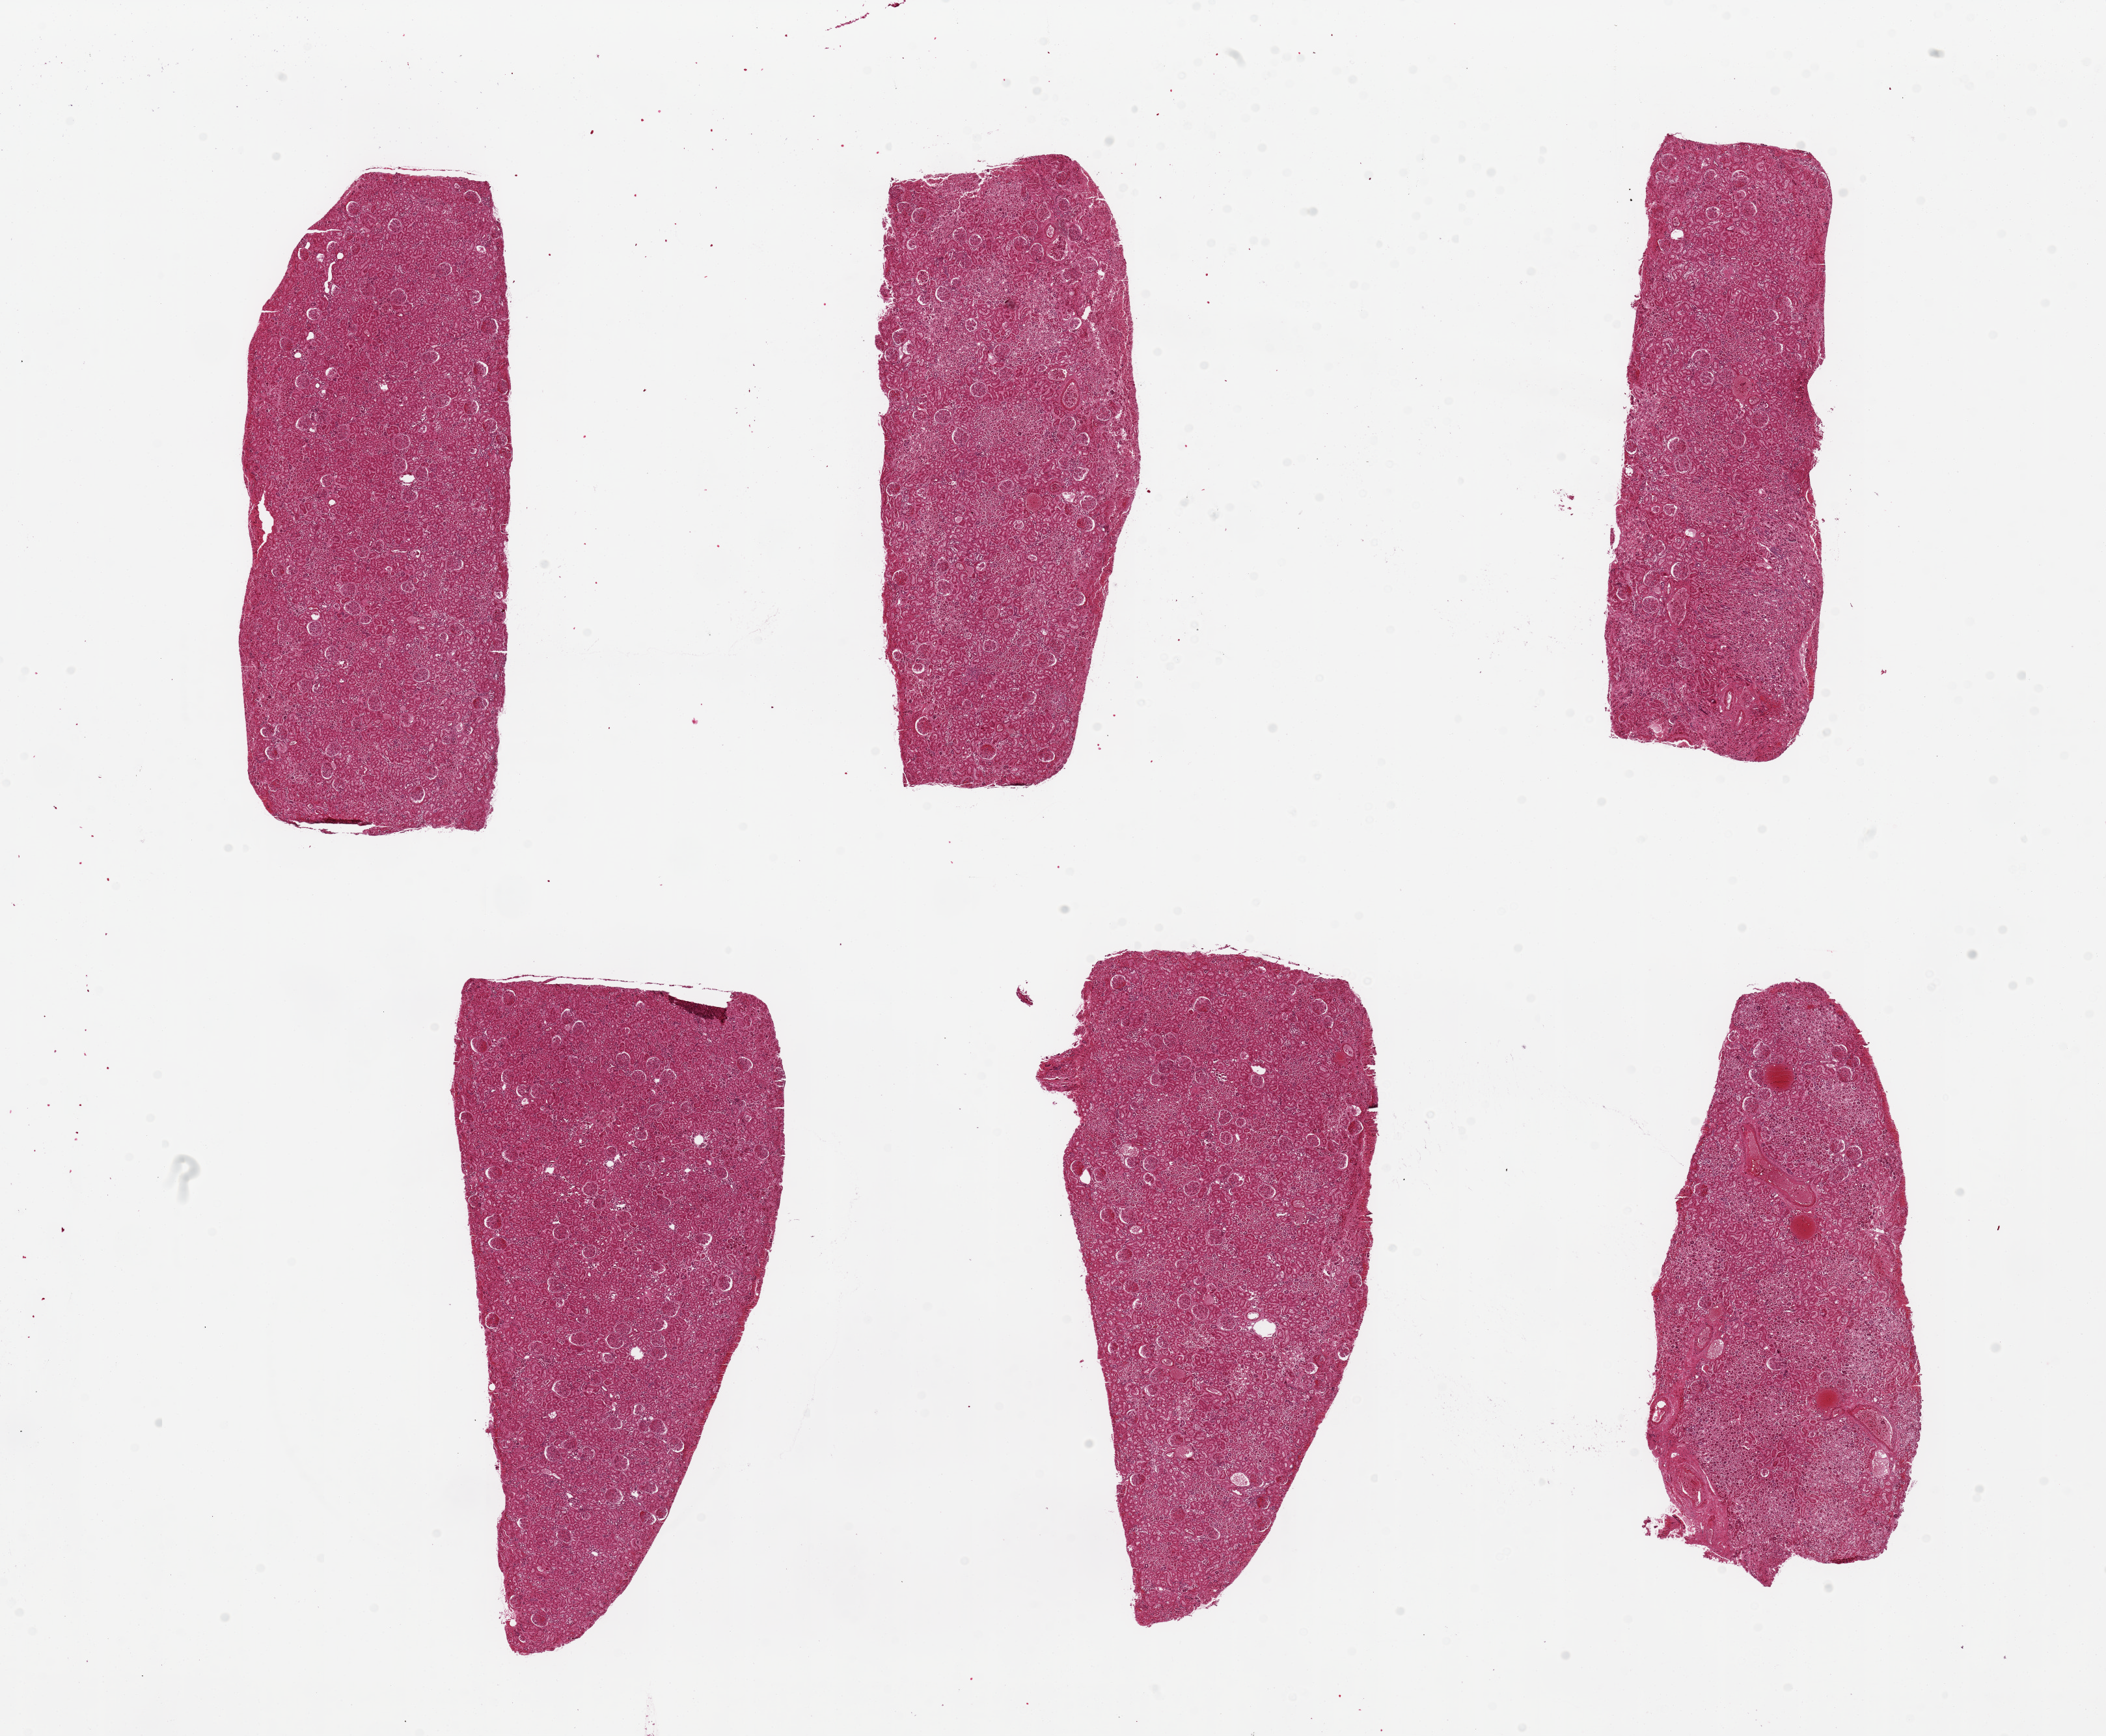
Digitized haematoxylin and eosin-stained section, a low-resolution overview of the entire scanned area, about 25.6 x 21.1 mm, PAXgene-fixed, paraffin-embedded tissue, sampled site (target tissue): renal cortex, donor tissue sample.
* pathologist's review note for this sample: 6 pieces, up to 8x4mm; glomeruli visible